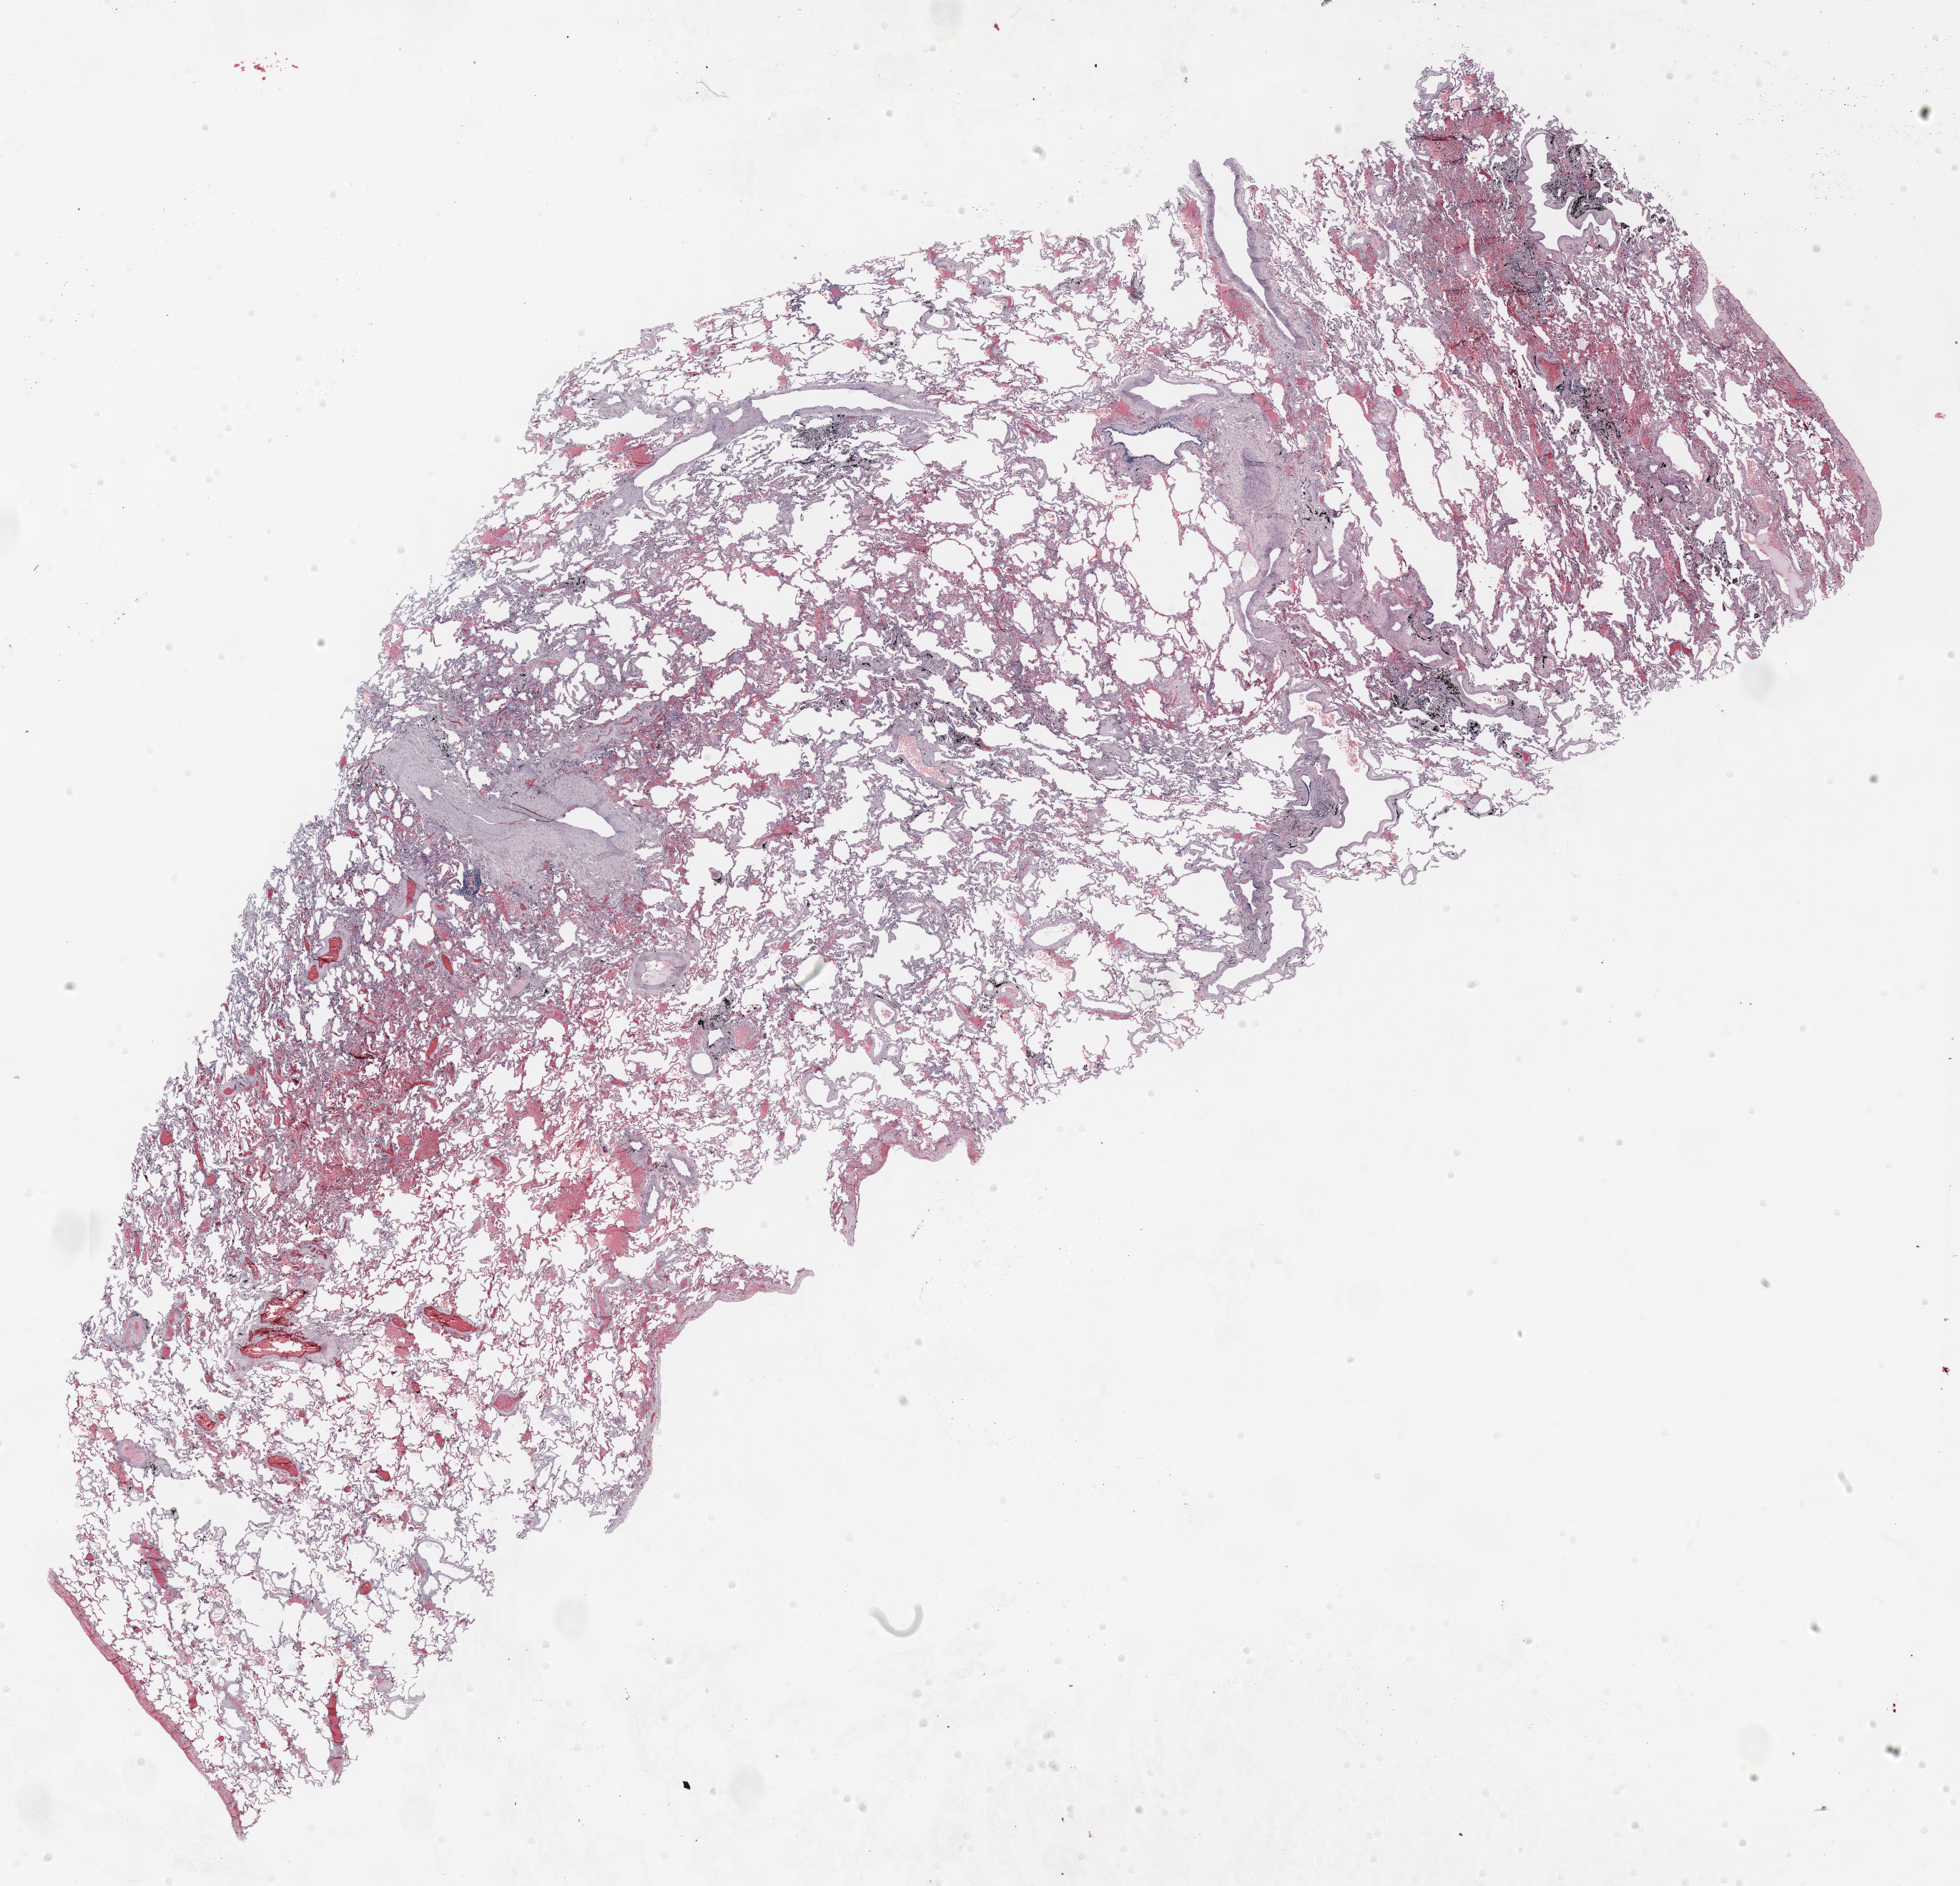
Whole-slide histology image, H&E-stained, shown as a low-resolution overview of the whole scanned area (about 22.0 x 21.2 mm), FFPE section, lung. Female patient, aged 58 at enrolment. Current smoker at enrolment. Grade: moderately differentiated (G2).
* tumour size (pathology): 7 mm
* stage (AJCC 6th edition): IA
* primary tumour location (clinical record): right upper lobe
* participant's lung-cancer diagnosis: Bronchiolo-alveolar adenocarcinoma, NOS (ICD-O-3 8250/3)